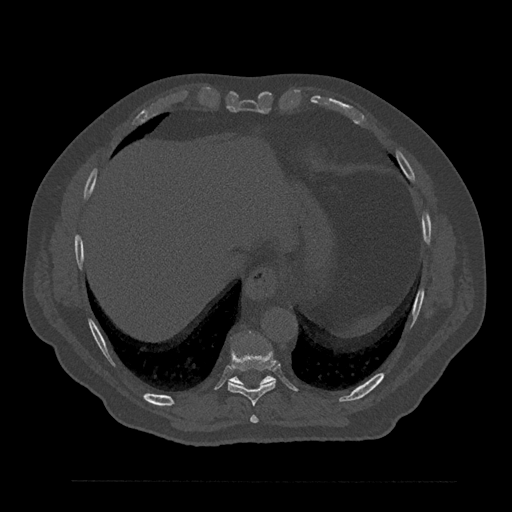
CT including the spine, one axial slice; position 390 of 797 along the scan axis; bone window (W 1800 / L 400 HU); 0.5 mm slice thickness; 512 × 512 image matrix, field of view 430 × 430 mm. Patient: male, 61 years. Case-level facts recorded for this patient, not image findings: primary cancer: prostate.
Structures marked on this image (semi-automatically segmented with operator editing):
- T10 vertebra: bounding box <228,376,274,387> (left, top, right, bottom; pixels)
- T8 vertebra: <250,415,258,424>
- T9 vertebra: <228,349,276,406>